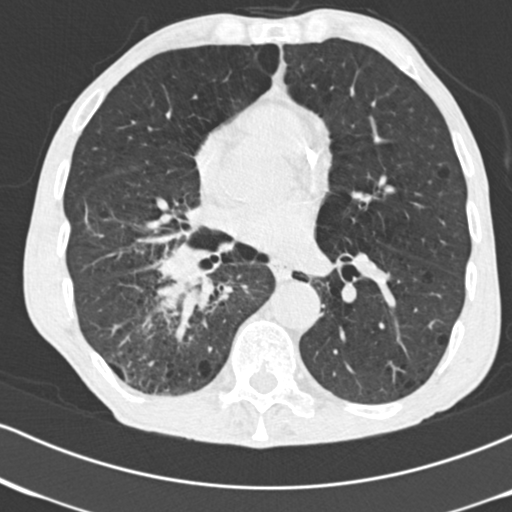
Low-dose screening chest CT, one axial slice; position 78 of 182 along the scan axis; reconstruction kernel B30f; 120 kVp; lung window (W 1500 / L -600 HU); 2 mm slice thickness; 512 × 512 image matrix, field of view 316 × 316 mm.
Annotated regions visible in this slice (outlined manually by an expert reader):
- lesion 1 (tumor, lower lobe of right lung): bounding box (x1, y1, x2, y2) in pixels: (153, 245, 216, 312)